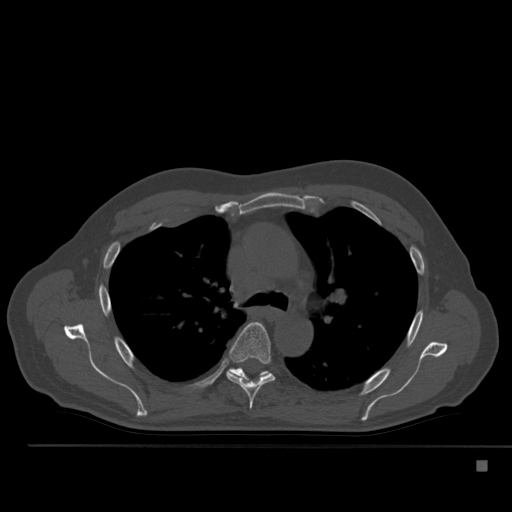
CT including the spine, one axial slice. Position 362 of 517 along the scan axis. Reconstruction kernel Br40s. Bone window (W 1800 / L 400 HU). 1.5 mm slice thickness. 512 × 512 image matrix. Male patient, age 70 years. Case-level facts recorded for this patient, not image findings: primary cancer: renal.
Structures marked on this image (semi-automatically segmented with operator editing):
- T5 vertebra: bounding box <226,322,275,410> (left, top, right, bottom; pixels)
- T6 vertebra: <228,368,270,381>